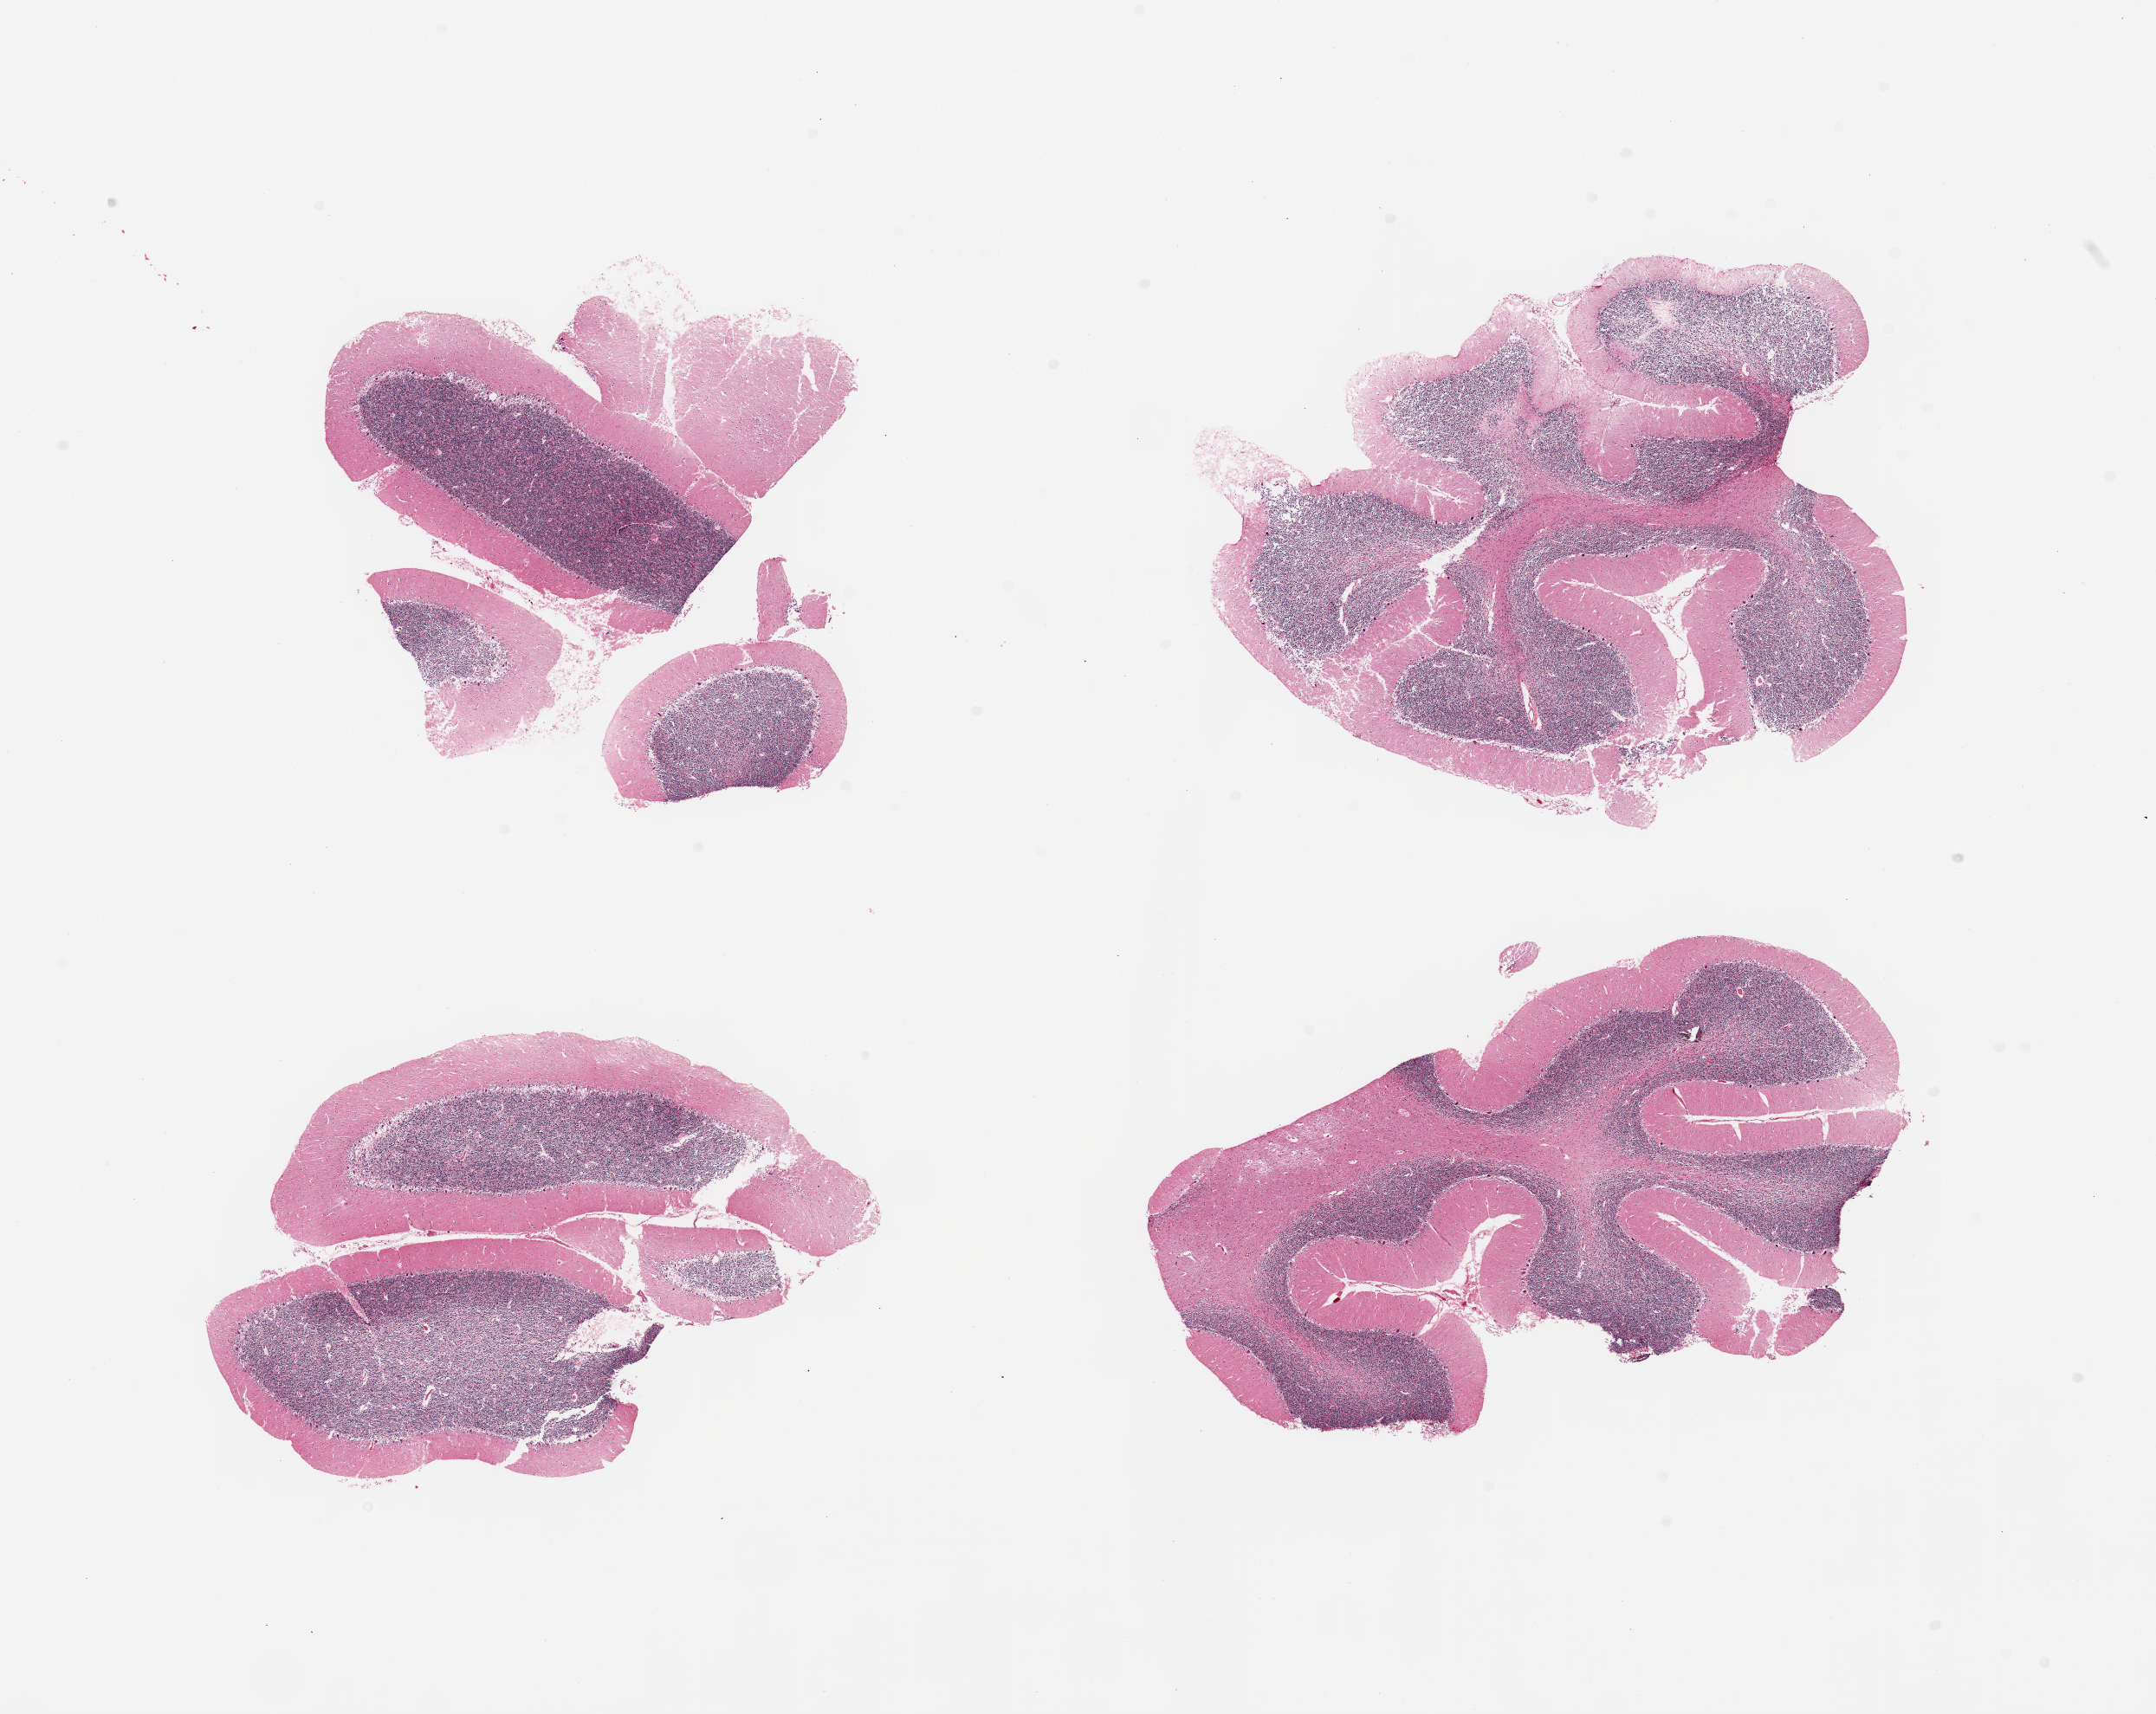
Whole-slide image, haematoxylin and eosin stain — a low-resolution overview of the entire scanned area, about 19.7 x 15.7 mm. PAXgene-fixed paraffin-embedded (PFPE) section. Sampled site (target tissue): cerebellum. Tissue donor sample. Donor: male.
- reviewer comment on this tissue sample: 4 pieces; Purkinje cells visualized, focal changes suggestive of hypoxia